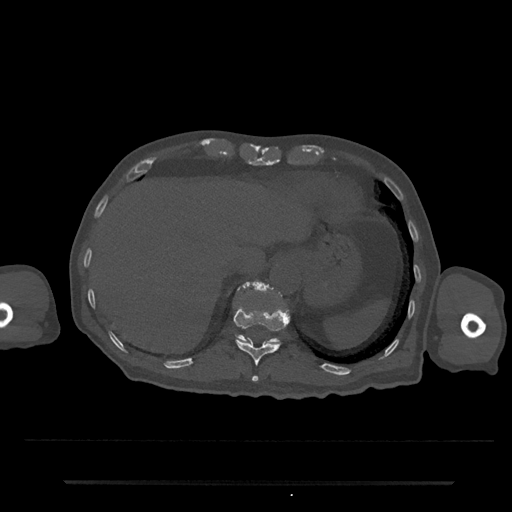
CT including the spine, one axial slice; position 243 of 797 along the scan axis; reconstruction kernel Br40s/3; 120 kVp; bone window (W 1800 / L 400 HU); 0.5 mm slice thickness; 512 × 512 image matrix, field of view 427 × 427 mm. Patient: male, 74 years. From the clinical record (not read from this slice): primary cancer: prostate.
Structures marked on this image (semi-automatically segmented with operator editing):
- T11 vertebra: box from (x=234, y=307) to (x=289, y=381) px
- T12 vertebra: (x=236, y=283)–(x=280, y=344)